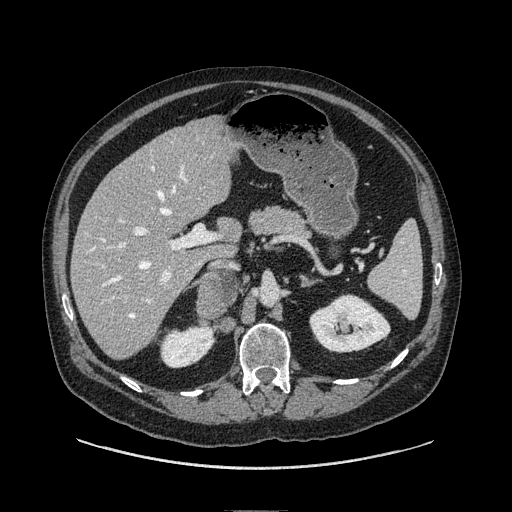
Contrast-enhanced abdominal CT, one axial slice. Slice 49 of 149 in the series (ordered by position). Soft-tissue window (W 400 / L 40 HU). 1.25 mm slice thickness. 512 × 512 image matrix. Male patient. Case-level facts recorded for this patient, not image findings: diagnosis: adrenocortical carcinoma; tumour side: right adrenal; tumour size at pathology: 7.5 cm; Ki-67 index: 15 %; stage (as recorded): 2.
Annotated regions visible in this slice (semi-automatically segmented with operator editing):
- mass: bounding box [x1, y1, x2, y2] px = [197, 274, 240, 314]